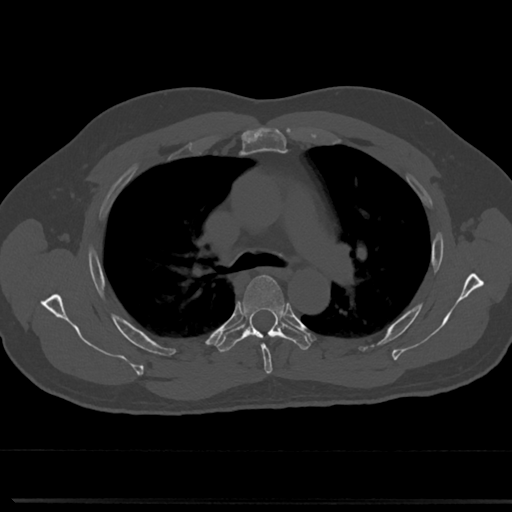
CT including the spine, one axial slice; slice 515 of 817 in the series (ordered by position); bone window (W 1800 / L 400 HU); 512 × 512 image matrix, field of view 355 × 355 mm. Male patient, age 61 years. From the clinical record (not read from this slice): primary cancer: prostate.
Outlined on this slice (semi-automatic segmentation, software-assisted and operator-edited):
- T4 vertebra: box from (x=243, y=275) to (x=287, y=370) px
- T5 vertebra: (x=219, y=299)–(x=310, y=351)